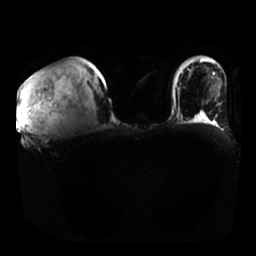
Breast MRI, one axial slice; slice 14 of 25 in the series (ordered by position); diffusion-weighted series; image 2 of 4 stored at this slice position (different b-values; order by instance number); 1.5 T; 4 mm slice thickness; 256 × 256 image matrix. Female patient.
Annotated regions visible in this slice (manually delineated by an expert):
- tumour on diffusion-weighted imaging: bounding box (x1, y1, x2, y2) in pixels: (19, 63, 61, 133)